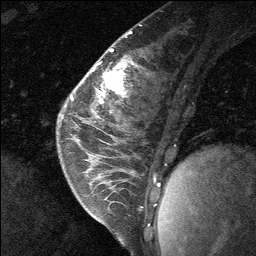
Breast MRI (dynamic contrast-enhanced), one sagittal slice. Slice 26 of 64 in the series (ordered by position). Dynamic contrast-enhanced study with each time point stored as its own series, time point 2 of 3 at this slice position (early post-contrast, ordered by acquisition time). 1.5 T. TE 4.8 ms, TR 27 ms. 256 × 256 image matrix. Female patient, age 26 years. Case-level facts recorded for this patient, not image findings: setting: breast cancer imaged before/during neoadjuvant chemotherapy; receptor status: HR-positive, HER2-negative.
Structures marked on this image (semi-automatic segmentation, software-assisted and operator-edited):
- analysis volume of interest (the breast-tissue region the enhancement analysis was run in; not a lesion): bounding box [x1, y1, x2, y2] px = [86, 43, 127, 138]
- tumour enhancement mask (voxels above the 90 % enhancement threshold inside the analysis volume of interest): [104, 72, 119, 89]